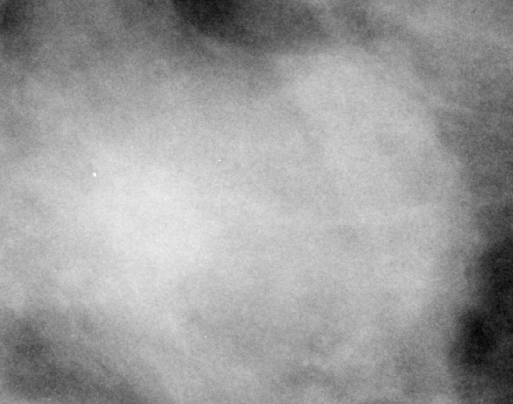
Region of interest cut from a scanned film mammogram (one marked finding); right breast; CC view.
Marked abnormality: mass, shape oval, margins obscured; BI-RADS assessment category 3; subtlety rating 5 on a 1 (subtle) to 5 (obvious) scale; benign without callback (not worked up further).